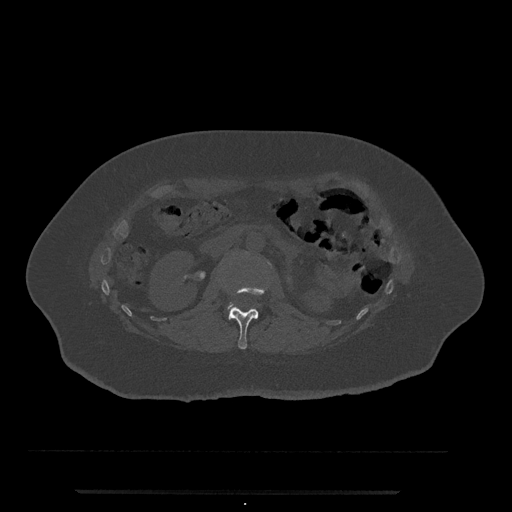
CT including the spine, one axial slice. Slice 80 of 797 in the series (ordered by position). 120 kVp. Bone window (W 1800 / L 400 HU). 512 × 512 image matrix, field of view 440 × 440 mm. Patient: female, 51 years. Case-level facts recorded for this patient, not image findings: primary cancer: neuro; vertebrae with lytic lesions (as recorded): T8.
Outlined on this slice (semi-automatically segmented with operator editing):
- L1 vertebra: bounding box <228,285,269,349> (left, top, right, bottom; pixels)
- L2 vertebra: <228,305,238,312>